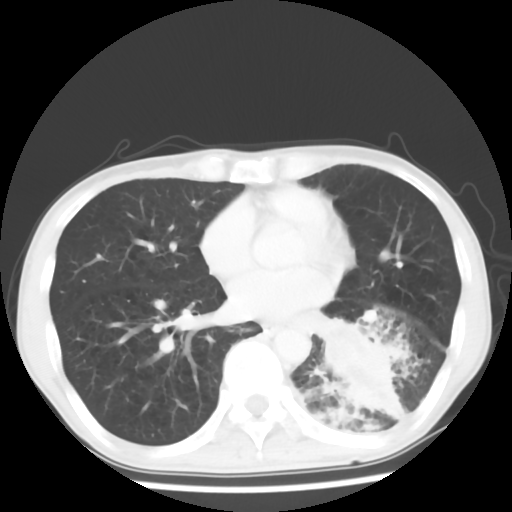
Chest CT, one axial slice; slice 26 of 64 in the series (ordered by position); 120 kVp; lung window (W 1500 / L -600 HU); 512 × 512 image matrix, field of view 313 × 313 mm. Patient: male, 68 years. Case-level facts recorded for this patient, not image findings: clinical TNM (as recorded): T4 N0 M0.
Annotated regions visible in this slice (bounding box drawn by a radiologist):
- lung tumour (recorded histology: squamous cell carcinoma): bounding box (x1, y1, x2, y2) in pixels: (307, 306, 415, 442)